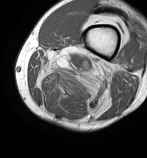
MRI of an extremity soft-tissue mass, one axial slice. Position 21 of 86 along the scan axis. MR volume resampled by the dataset authors to the PET/CT grid (not the native acquisition matrix). 3.27 mm slice thickness. 147 × 158 image matrix, field of view 144 × 154 mm. Male patient. Case-level facts recorded for this patient, not image findings: histological type: undifferentiated pleomorphic liposarcoma; grade: high; site of the primary tumour: left thigh.
Structures marked on this image (expert contour drawn on MRI and transferred to this co-registered scan by the dataset authors):
- gross tumour volume including surrounding oedema: bounding box [x1, y1, x2, y2] px = [35, 46, 122, 118]